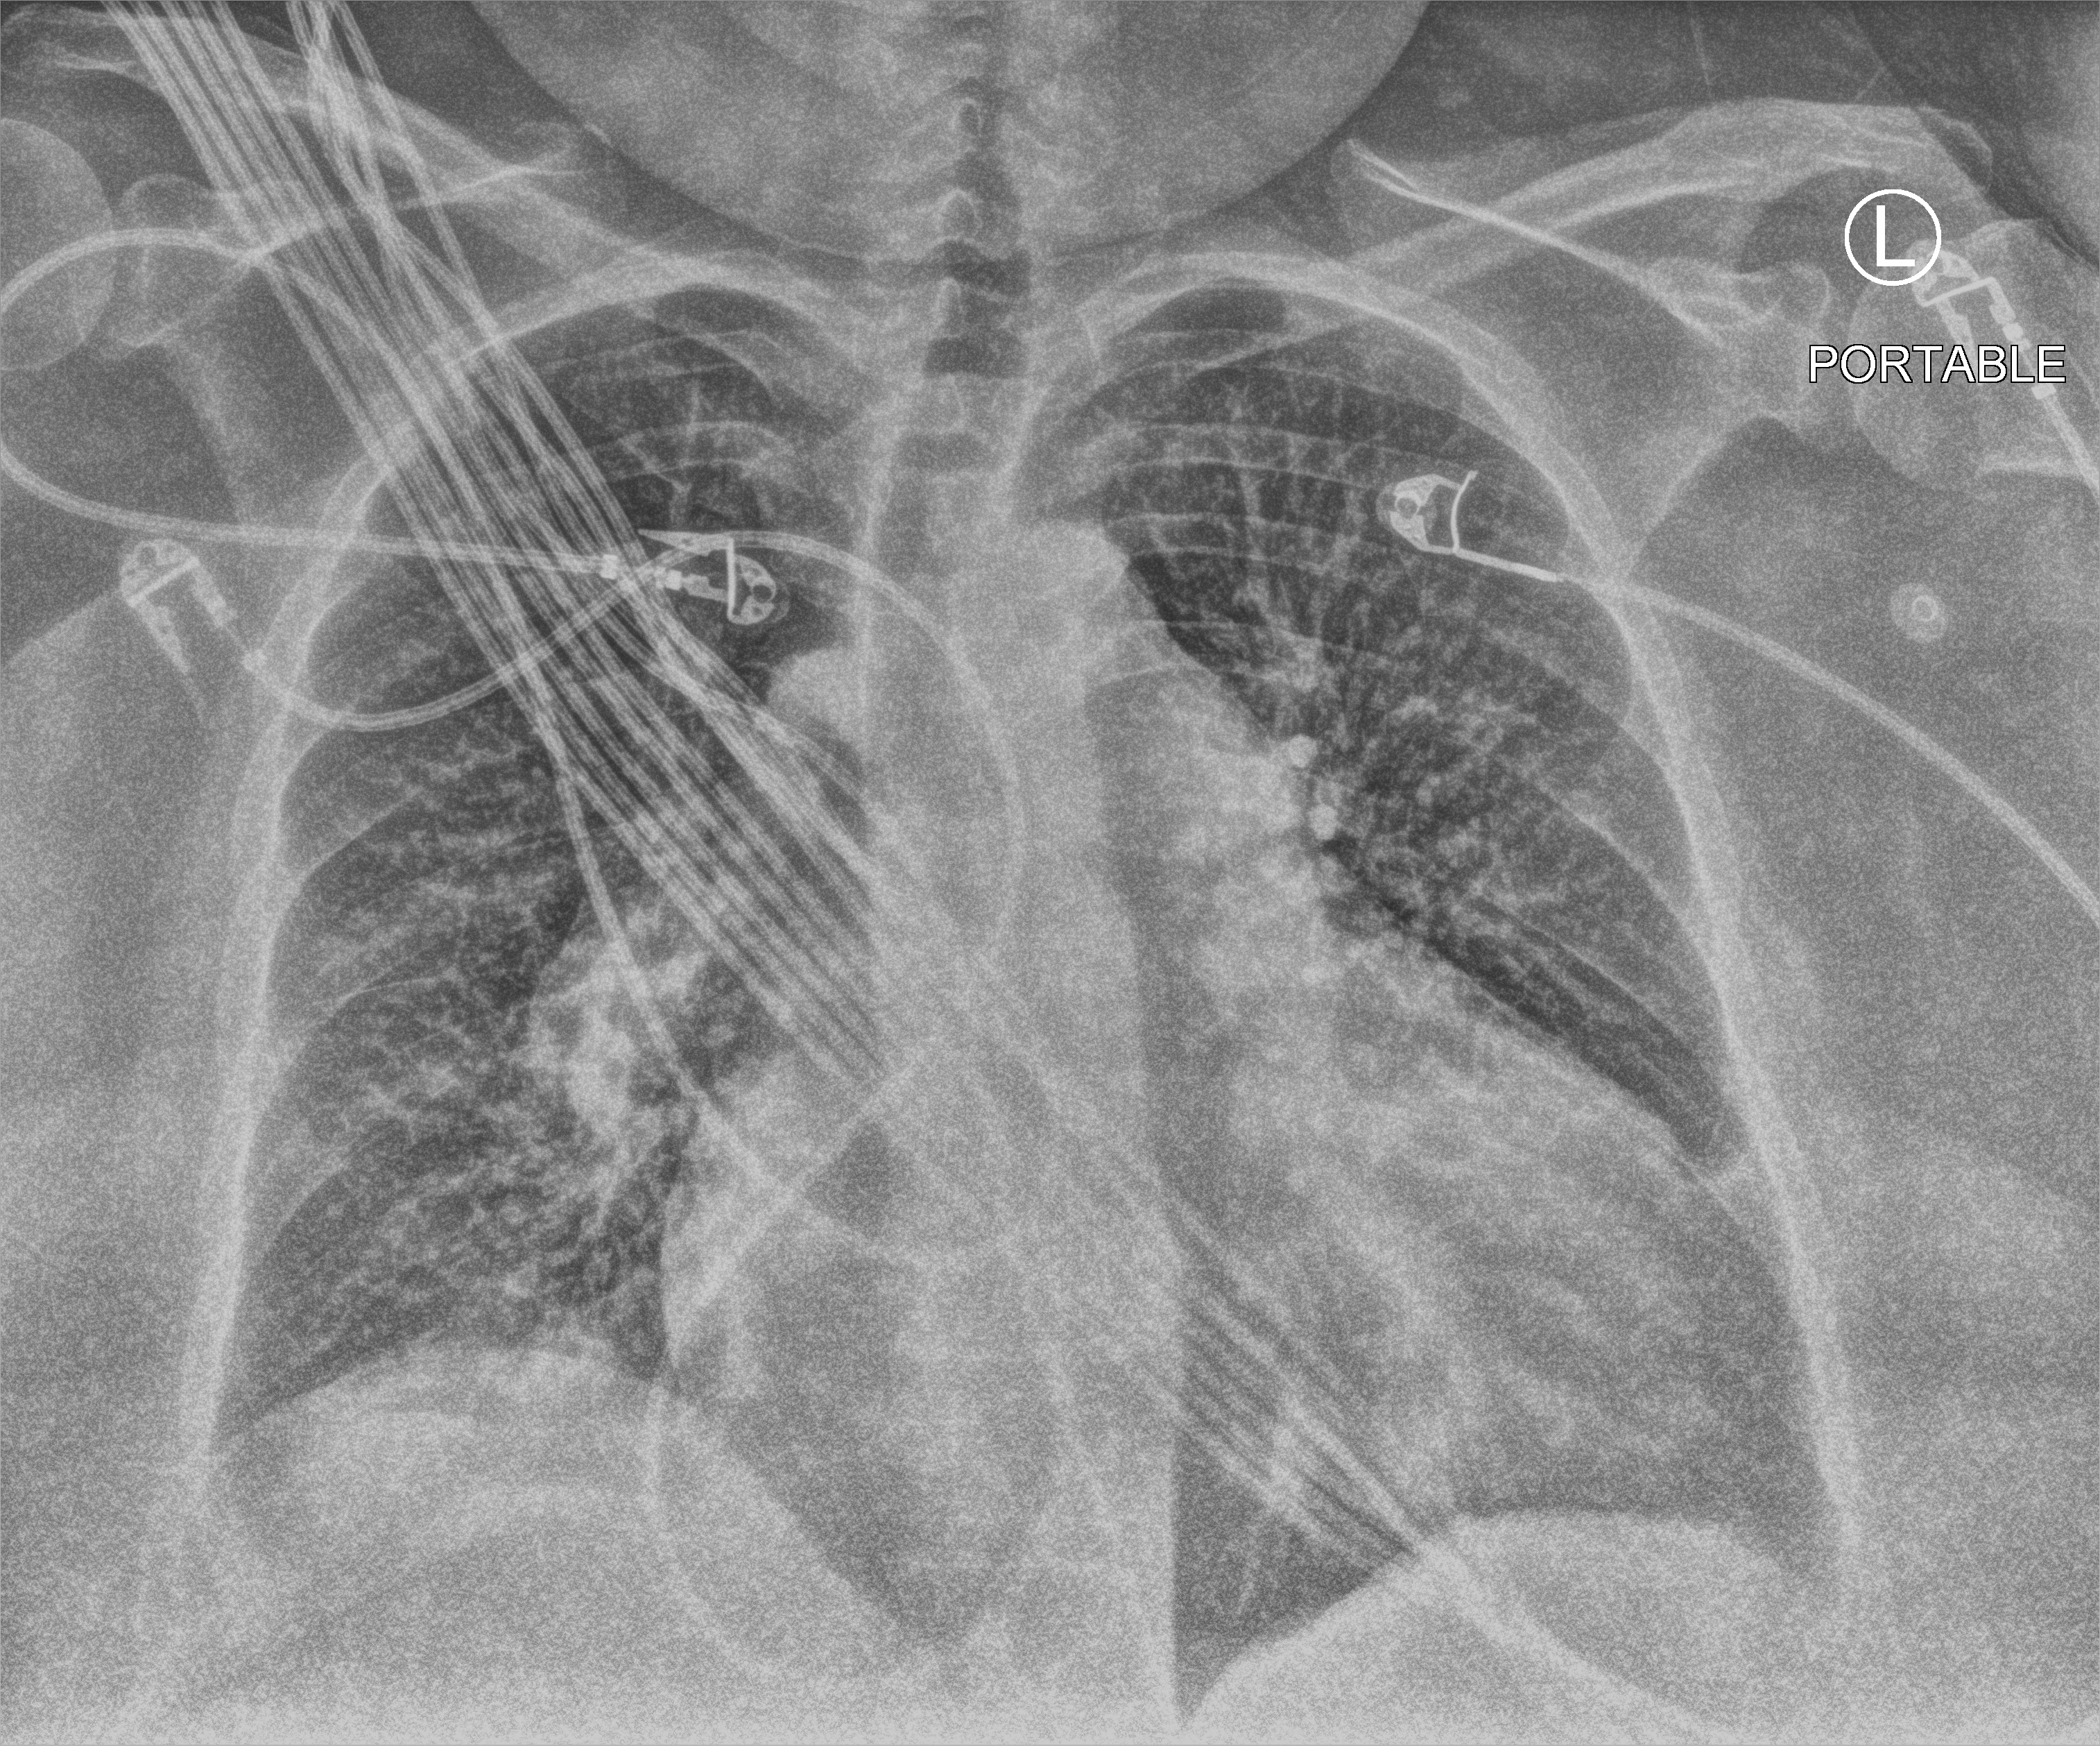
Bedside chest radiograph (computed radiography); anteroposterior (AP) projection. Female patient hospitalised with COVID-19, age 60–74 years.
From the hospital-stay record, not from the radiograph (when in the stay this image was taken is not recorded): mechanically ventilated during this hospital stay: yes; length of hospital stay: 6 days; admitted to intensive care during this hospital stay: yes.